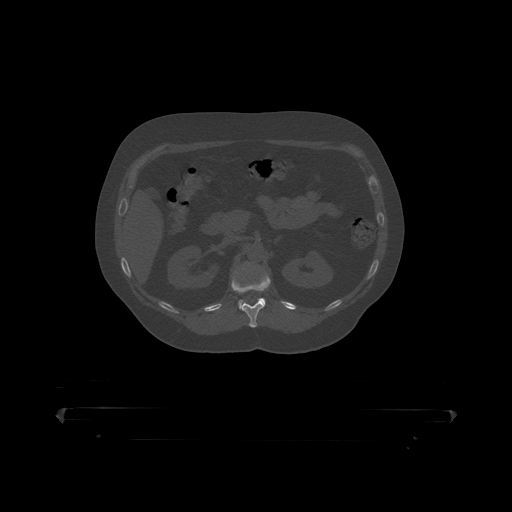
CT including the spine, one axial slice. Slice 161 of 390 in the series (ordered by position). Reconstruction kernel STANDARD. Bone window (W 1800 / L 400 HU). 1.25 mm slice thickness. 512 × 512 image matrix. Male patient, age 60 years. Case-level facts recorded for this patient, not image findings: primary cancer: prostate.
Outlined on this slice (semi-automatically segmented with operator editing):
- L1 vertebra: bounding box (x1, y1, x2, y2) in pixels: (239, 299, 266, 309)
- T12 vertebra: (232, 271, 271, 319)